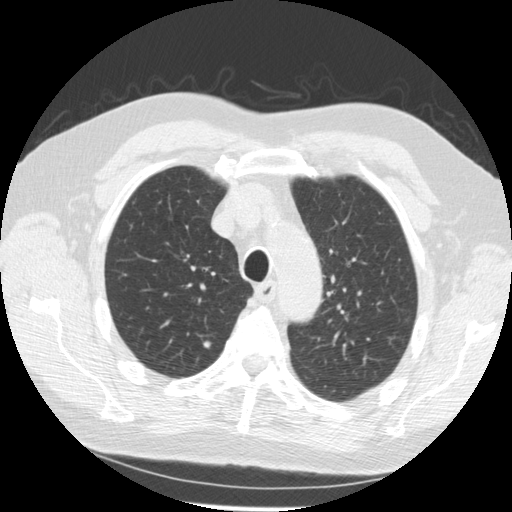
Low-dose screening chest CT, one axial slice; position 205 of 259 along the scan axis; 120 kVp; lung window (W 1500 / L -600 HU); 512 × 512 image matrix.
Annotated regions visible in this slice (outlined manually by an expert reader):
- lesion 1 (nodule, upper lobe of right lung): bounding box <202,341,212,350> (left, top, right, bottom; pixels)